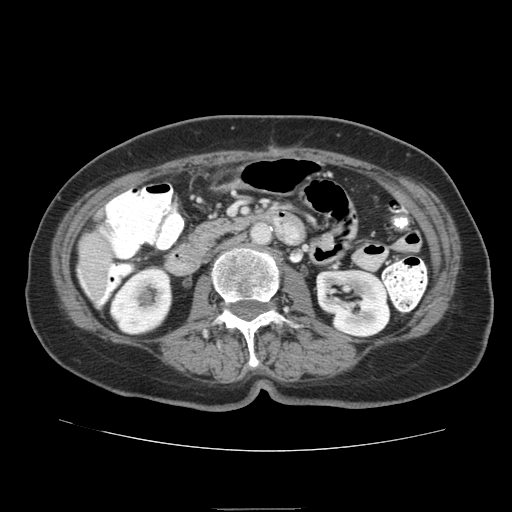
Contrast-enhanced abdominal CT (liver protocol), one axial slice. Slice 22 of 95 in the series (ordered by position). Soft-tissue window (W 400 / L 40 HU). 512 × 512 image matrix, field of view 360 × 360 mm. Case-level facts recorded for this patient, not image findings: diagnosis: hepatocellular carcinoma (patient treated with transarterial chemoembolisation; whether this scan precedes or follows treatment is not stated here); TNM stage (as recorded): Stage-IVA; Child-Pugh class: B.
Outlined on this slice (semi-automatic segmentation, software-assisted and operator-edited):
- liver parenchyma outside the tumour (the mass and vessels are separate outlines, so this box may not span the whole liver): bounding box (x1, y1, x2, y2) in pixels: (76, 224, 112, 307)
- liver vessels: (81, 231, 109, 304)